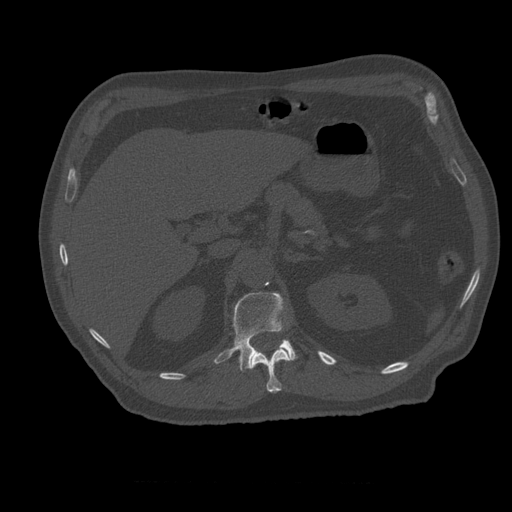
CT including the spine, one axial slice. Slice 248 of 399 in the series (ordered by position). Reconstruction kernel STANDARD. Bone window (W 1800 / L 400 HU). 512 × 512 image matrix, field of view 407 × 407 mm. Patient age 73 years. From the clinical record (not read from this slice): primary cancer: prostate; vertebrae with lytic lesions (as recorded): L2.
Outlined on this slice (semi-automatic segmentation, software-assisted and operator-edited):
- L1 vertebra: bounding box (x1, y1, x2, y2) in pixels: (214, 293, 297, 371)
- T12 vertebra: (249, 349, 290, 393)